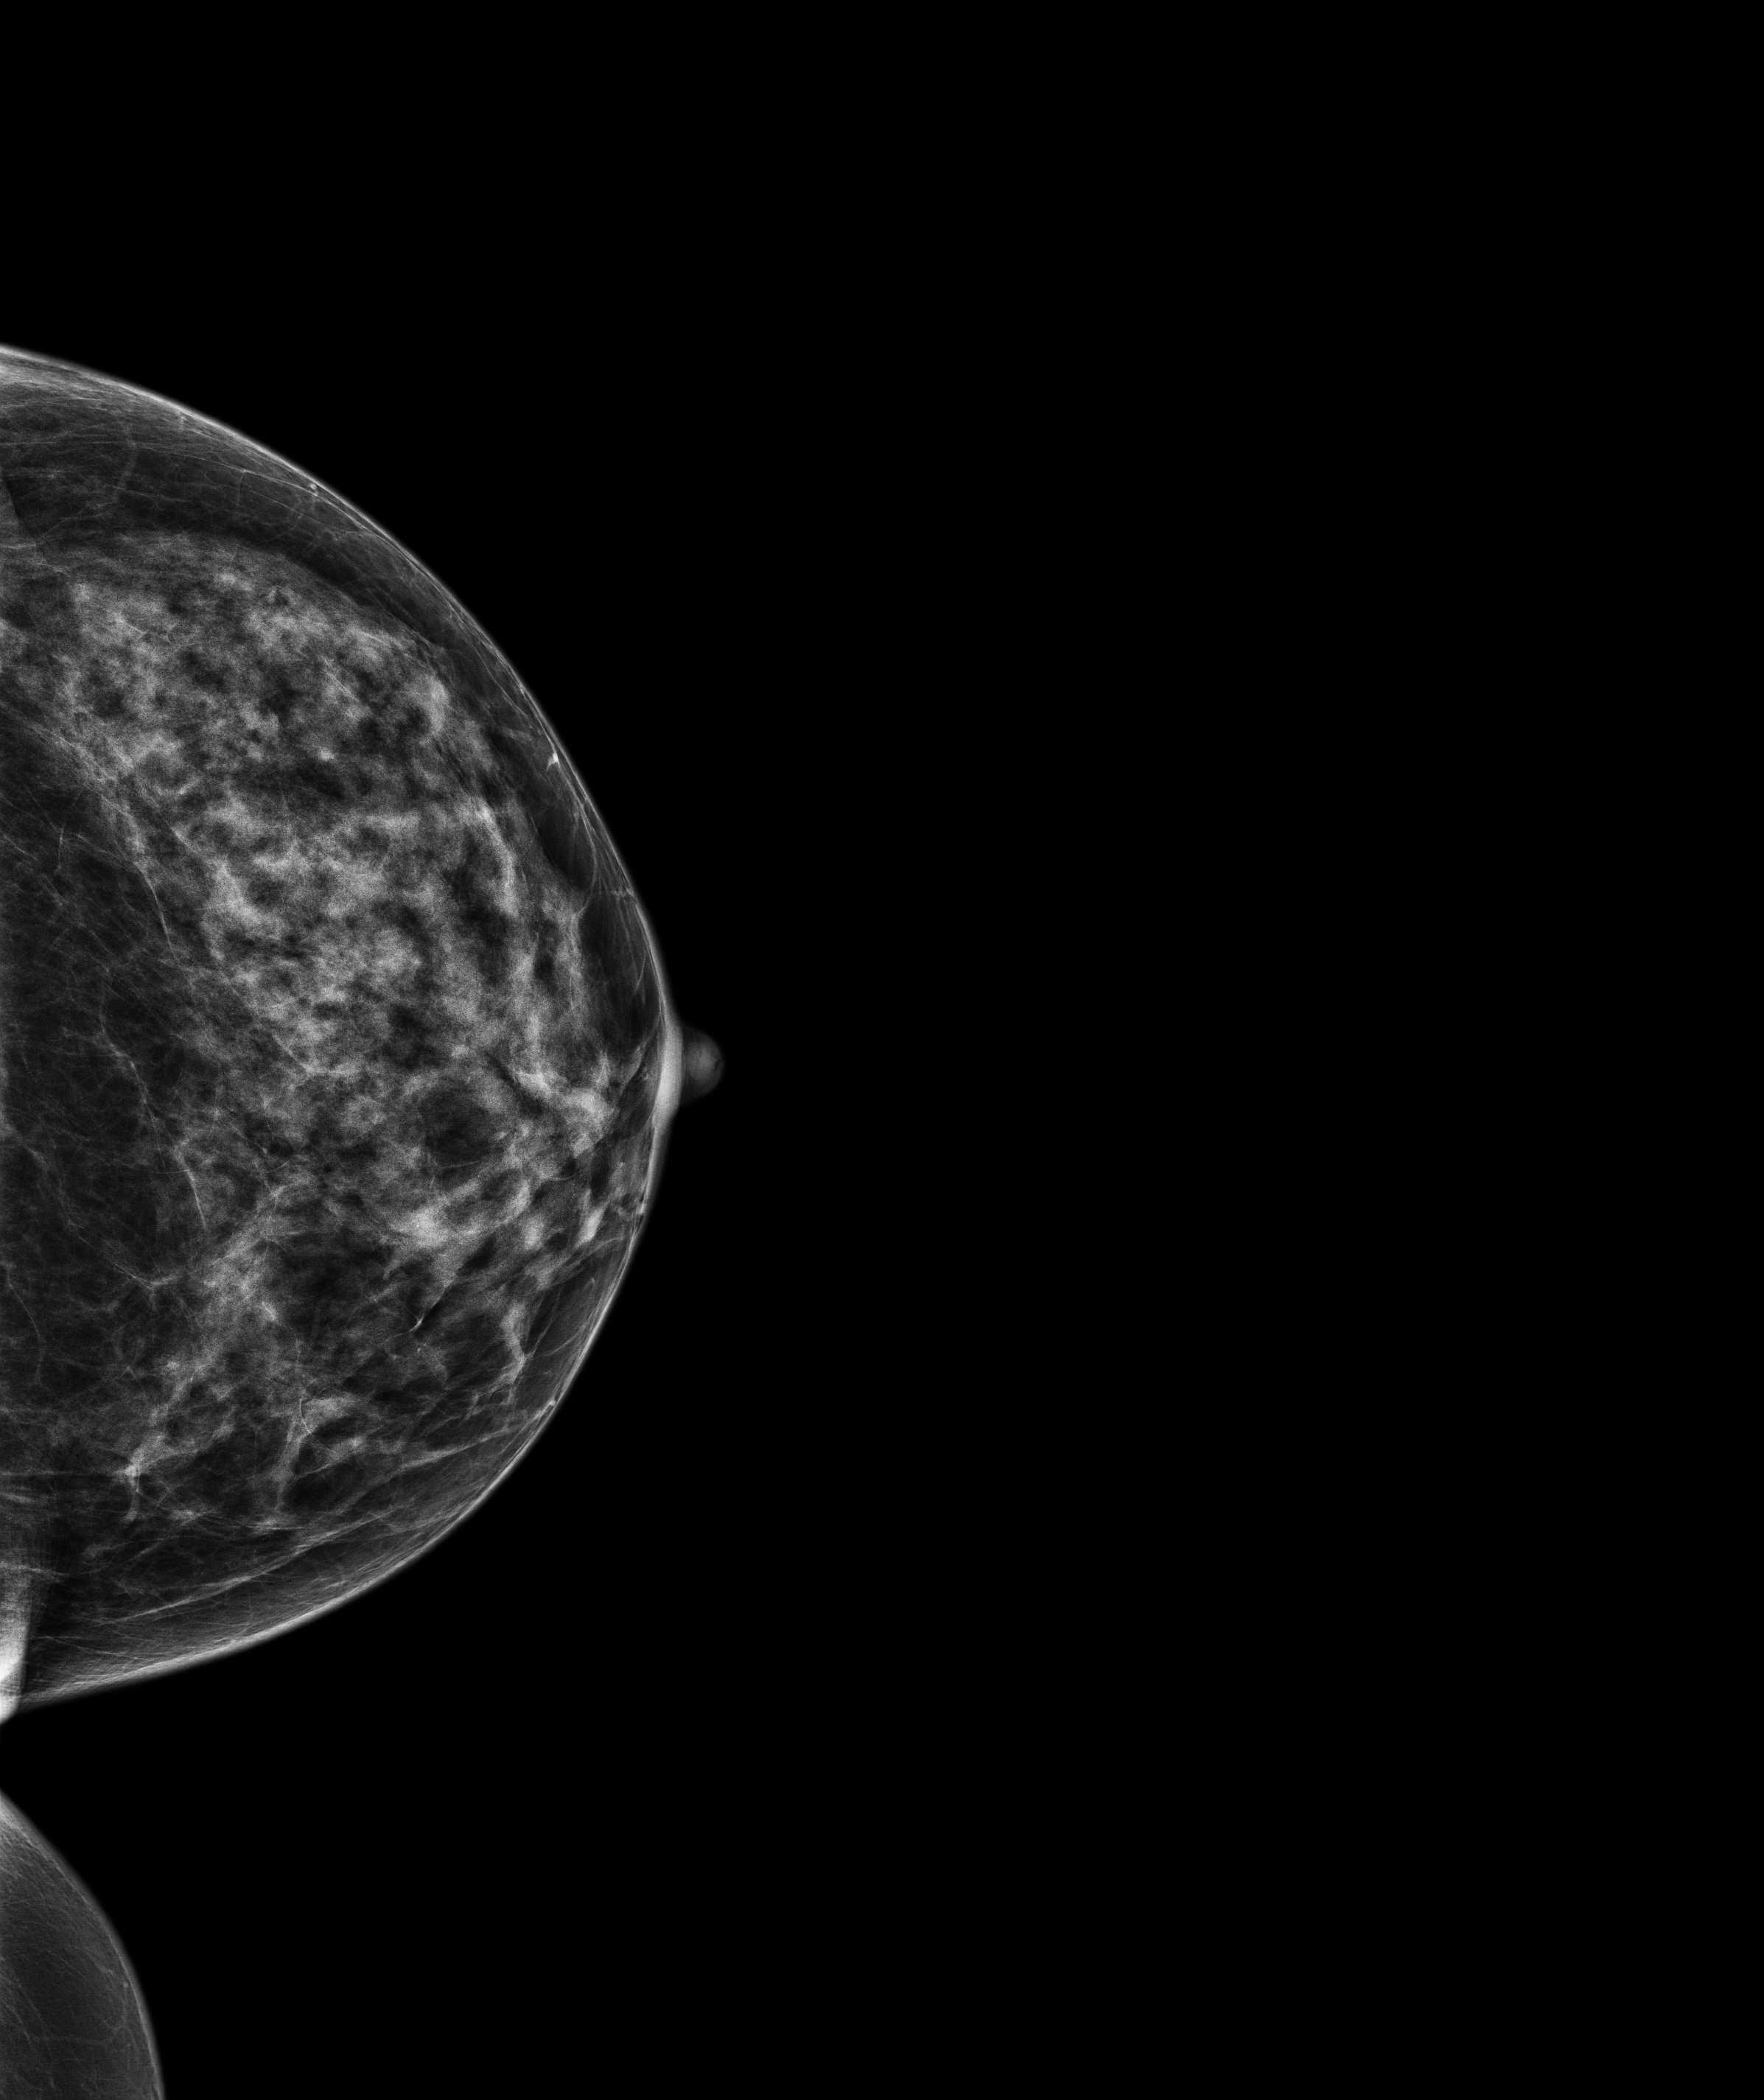
Screening examination. Patient: female, 59 years.
Image type: full-field digital mammogram. Breast: left. Projection: CC view.